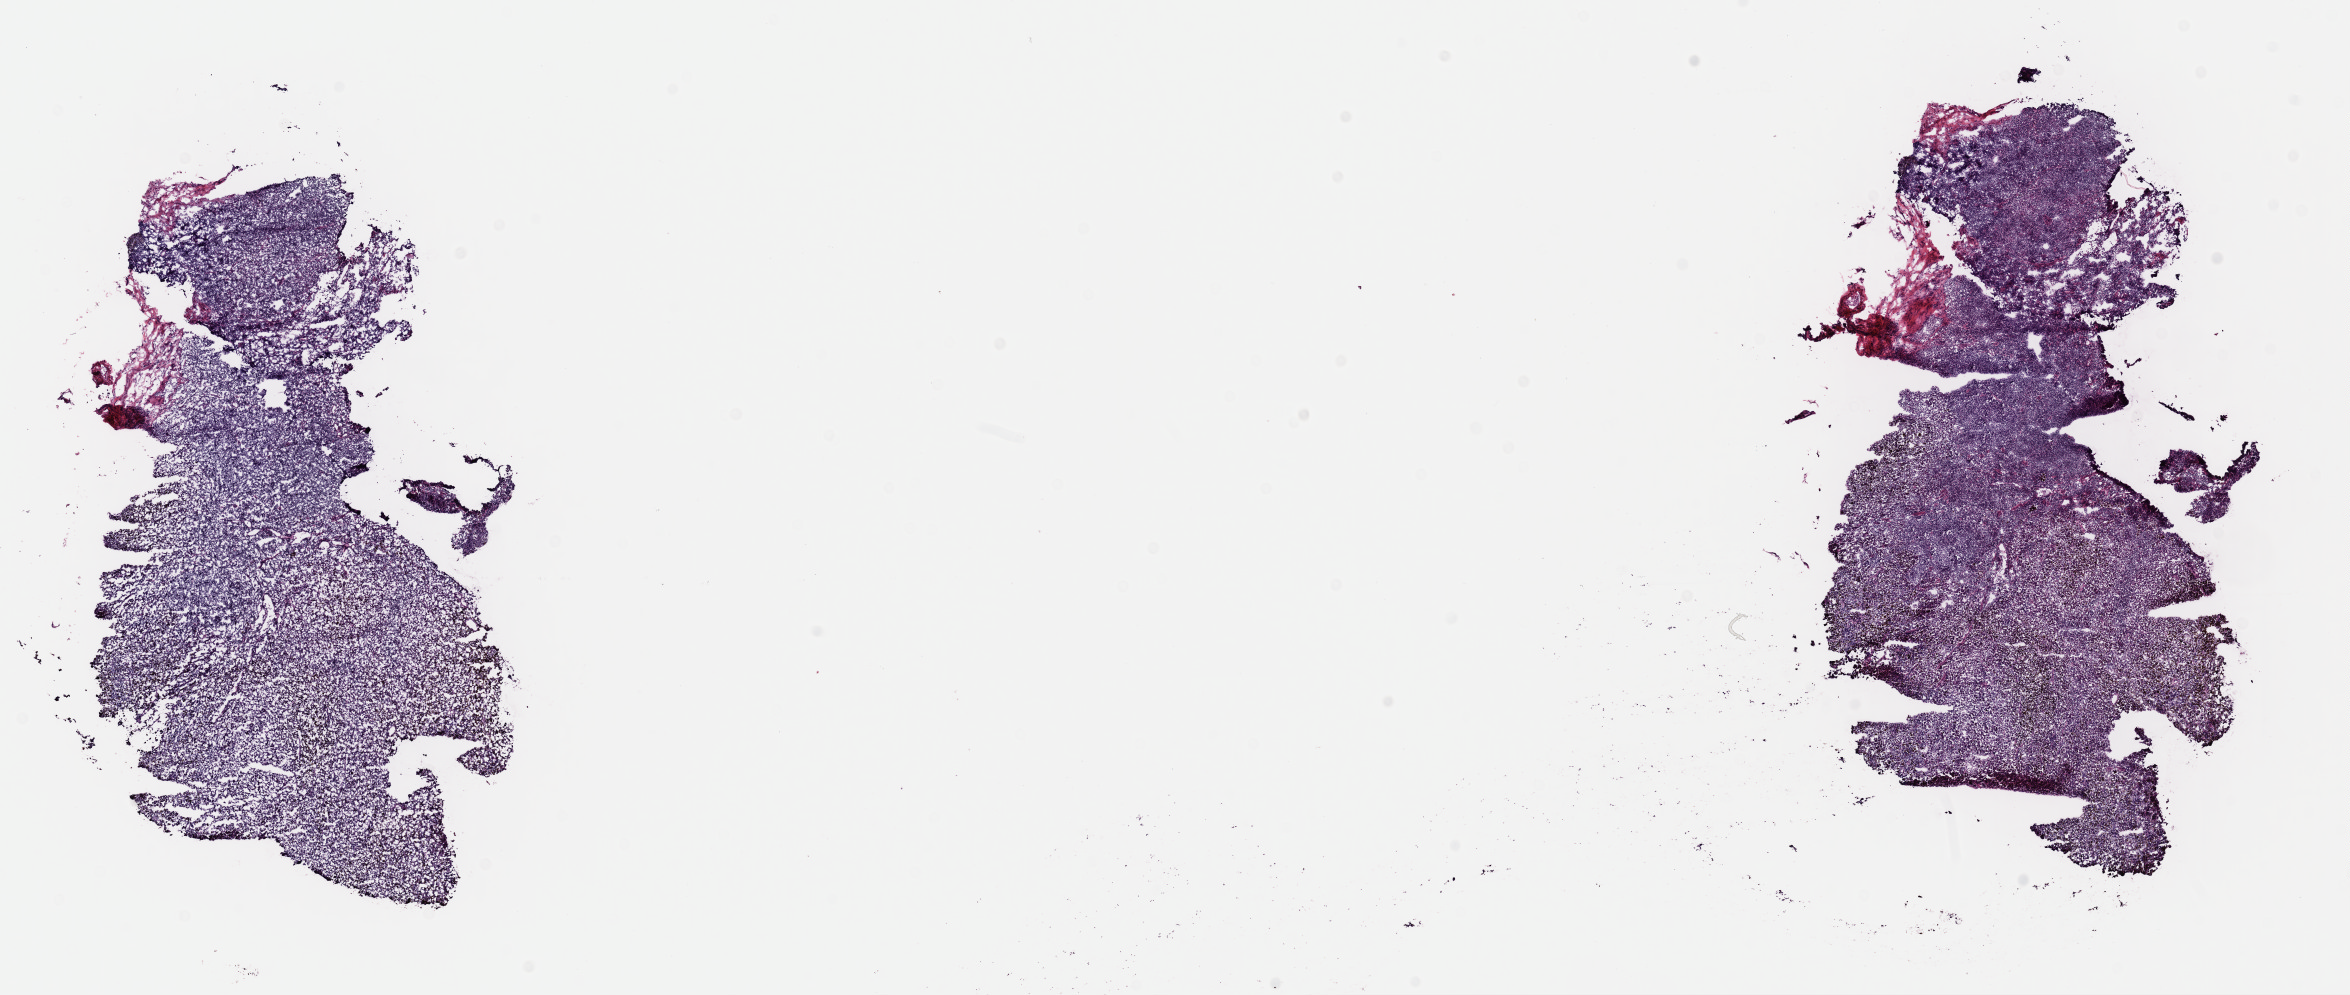
Digitized H&E-stained tissue section (whole slide) — a low-resolution overview of the entire scanned area, about 18.6 x 7.9 mm. Frozen section from the top of the tissue portion. Metastatic tumour sample, sampled site not recorded. Female, age 70 years at initial diagnosis. Slide review estimates, as recorded: tumour cells 70%, tumour nuclei 70%, normal cells 0%, stromal cells 30%, necrosis 0%. Inflammatory infiltration, as recorded: lymphocyte infiltration 20%, monocyte infiltration 0%, neutrophil infiltration 0%.
- this section: metastatic tumour tissue
- patient diagnosis: Malignant melanoma, NOS